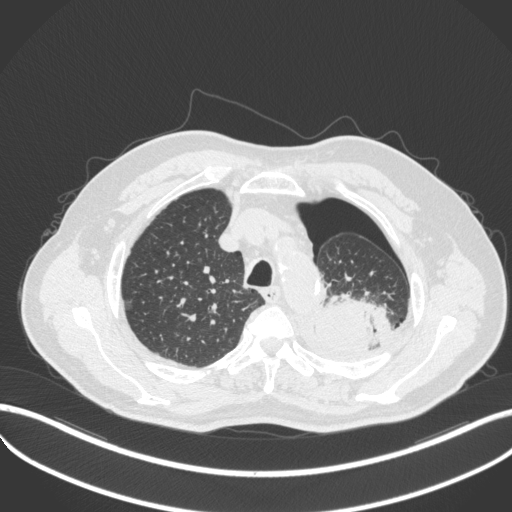
Chest CT, one axial slice. Slice 400 of 466 in the series (ordered by position). 120 kVp. Lung window (W 1500 / L -600 HU). 1 mm slice thickness. 512 × 512 image matrix, field of view 400 × 400 mm. Patient: male, 76 years. Case-level facts recorded for this patient, not image findings: clinical TNM (as recorded): T3 N0 M1b.
Structures marked on this image (rectangle marked by the reading radiologist):
- lung tumour (recorded histology: adenocarcinoma): bounding box (x1, y1, x2, y2) in pixels: (312, 288, 386, 353)